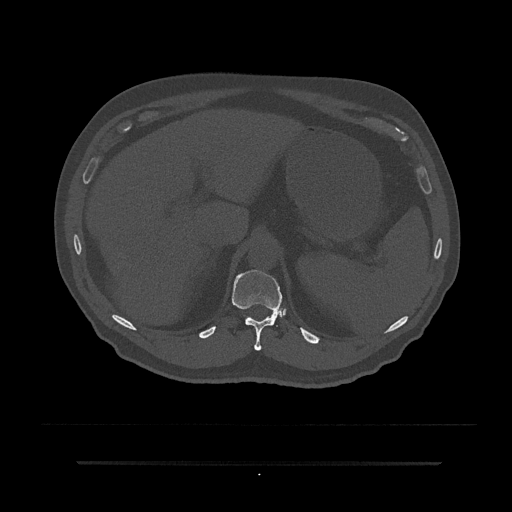
CT including the spine, one axial slice; slice 261 of 797 in the series (ordered by position); reconstruction kernel Br40s/3; bone window (W 1800 / L 400 HU); 0.5 mm slice thickness; 512 × 512 image matrix, field of view 464 × 464 mm. Male patient, age 59 years. Case-level facts recorded for this patient, not image findings: primary cancer: bile ducts; vertebrae with lytic lesions (as recorded): T10.
Outlined on this slice (semi-automatic segmentation, software-assisted and operator-edited):
- T11 vertebra: bounding box <232,269,284,351> (left, top, right, bottom; pixels)